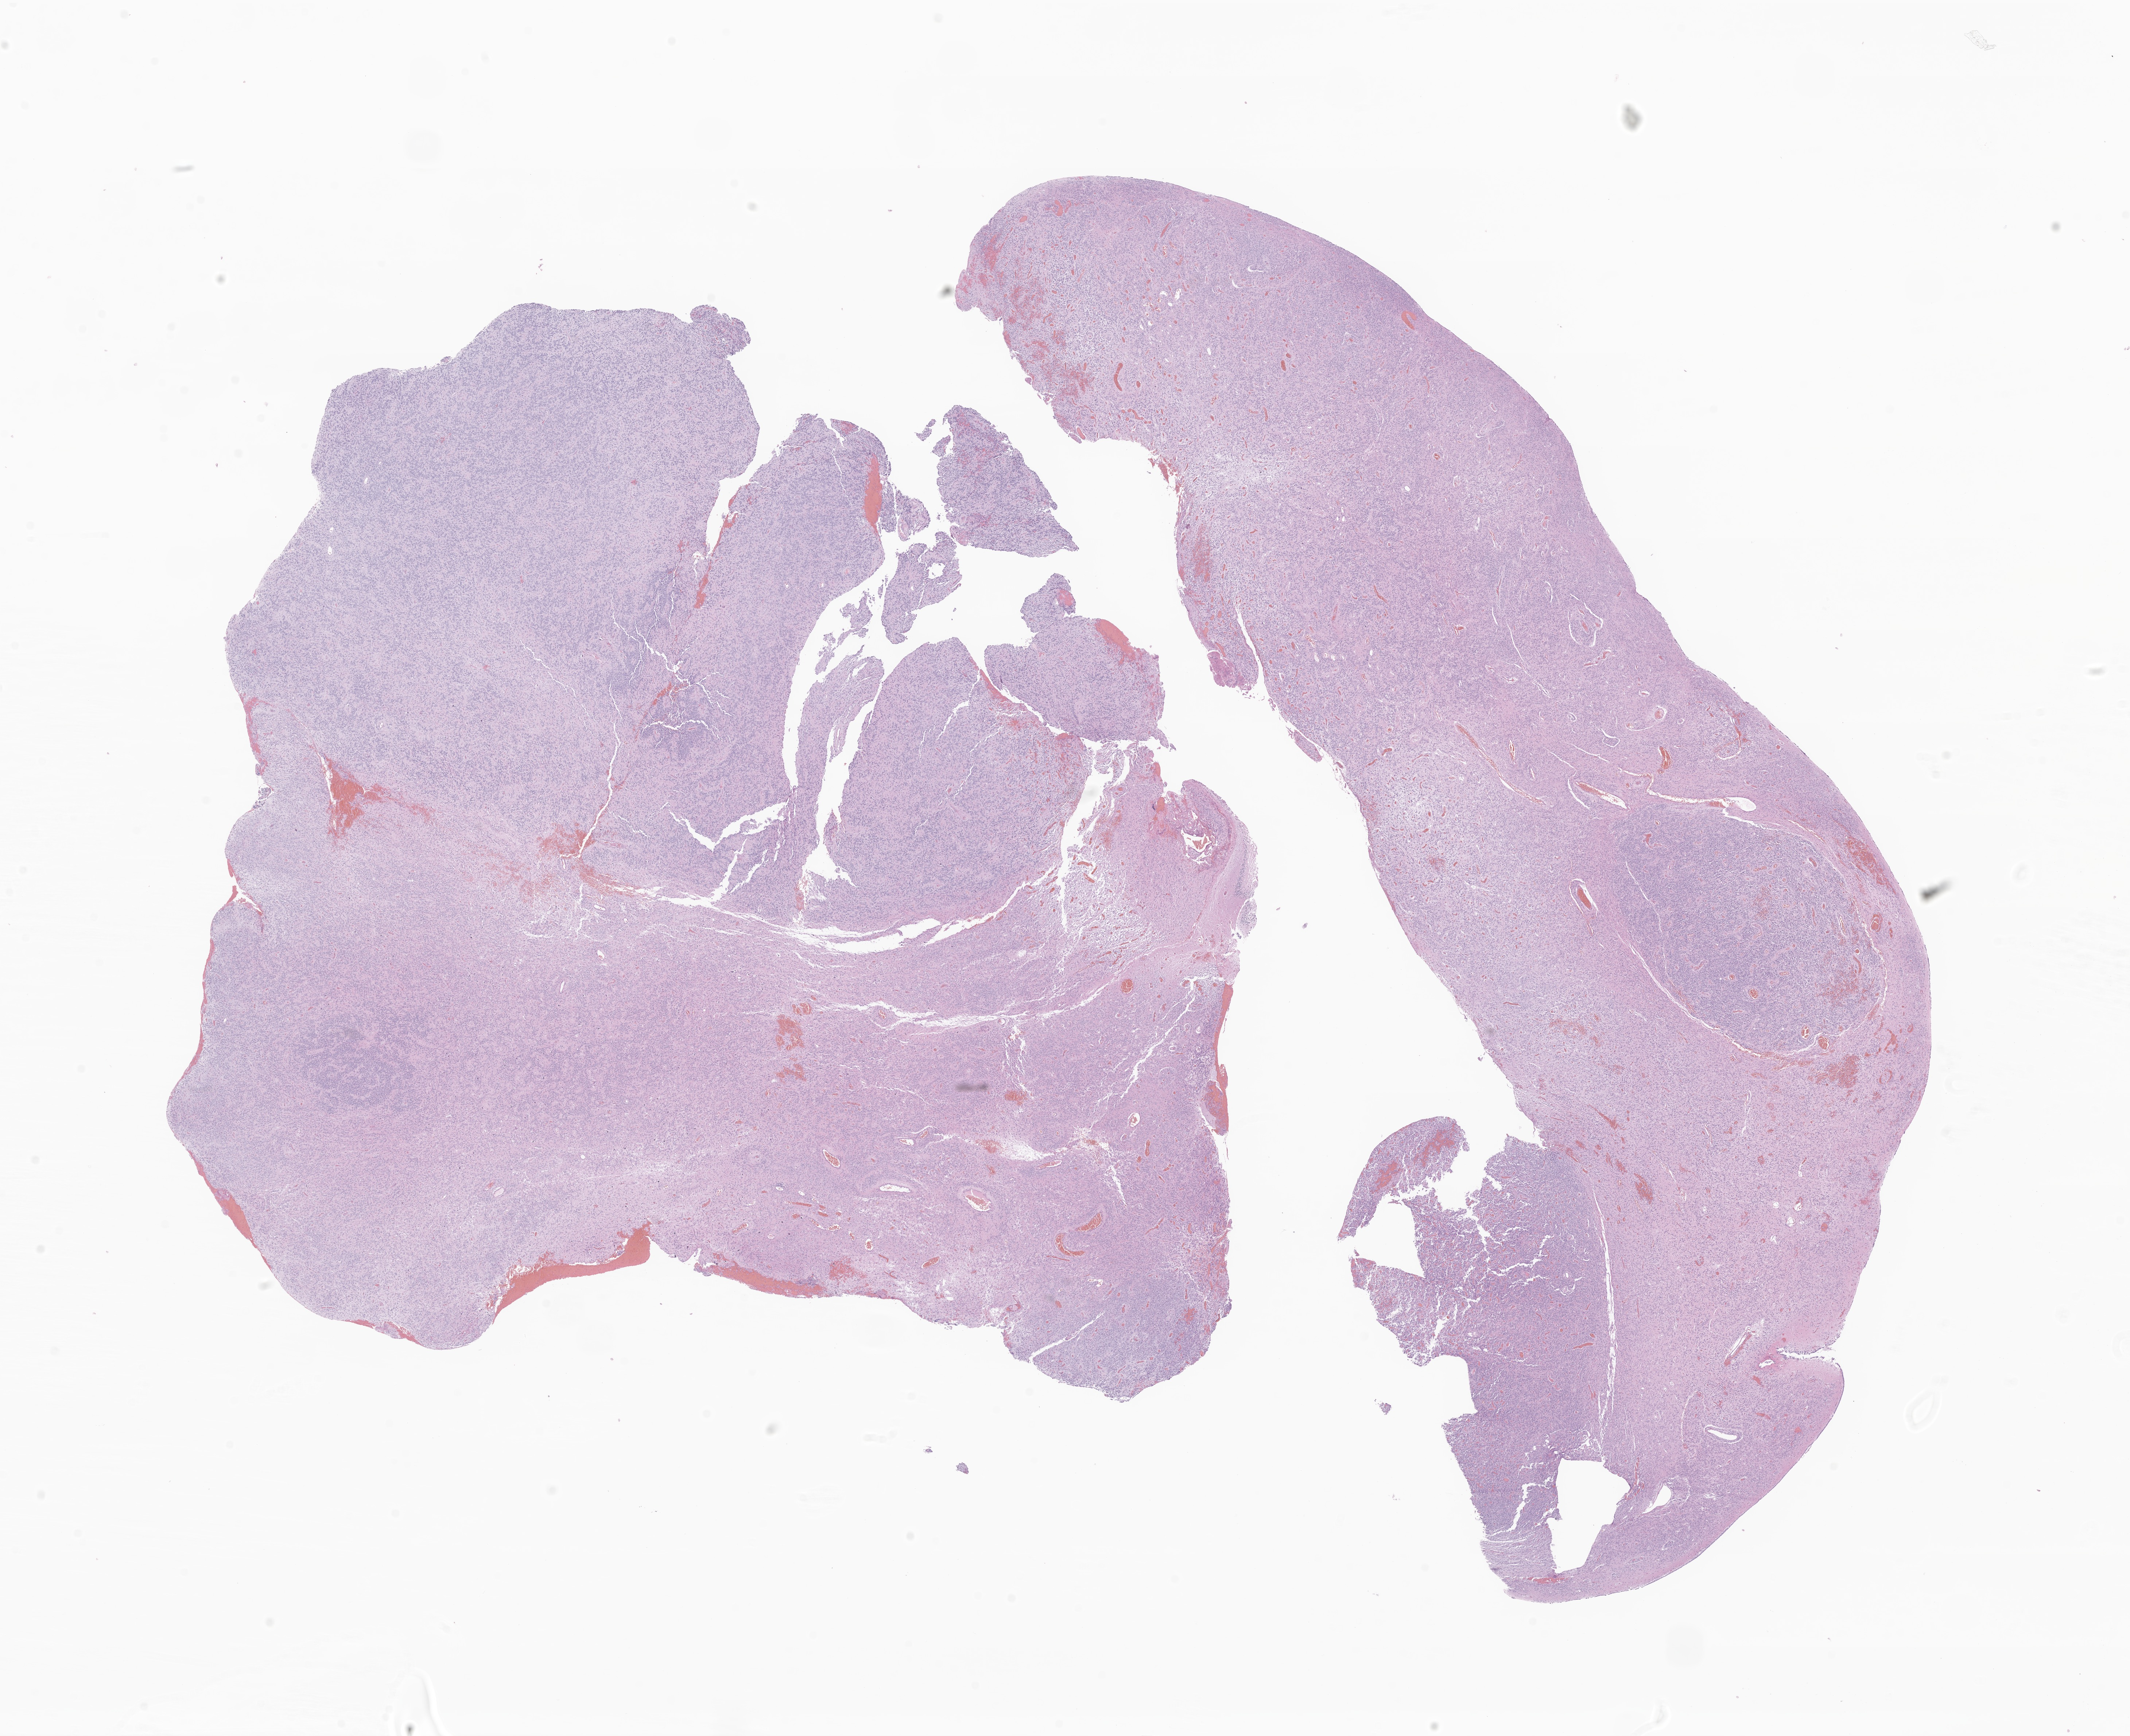
H&E whole-slide image of tumor tissue from the brain, shown as a low-resolution overview of the whole scanned area (about 24.6 x 20.1 mm); formalin-fixed paraffin-embedded section. Patient: female, age 40 months (3 years 4 months).
Recorded diagnosis: Neoplasm, uncertain whether benign or malignant.